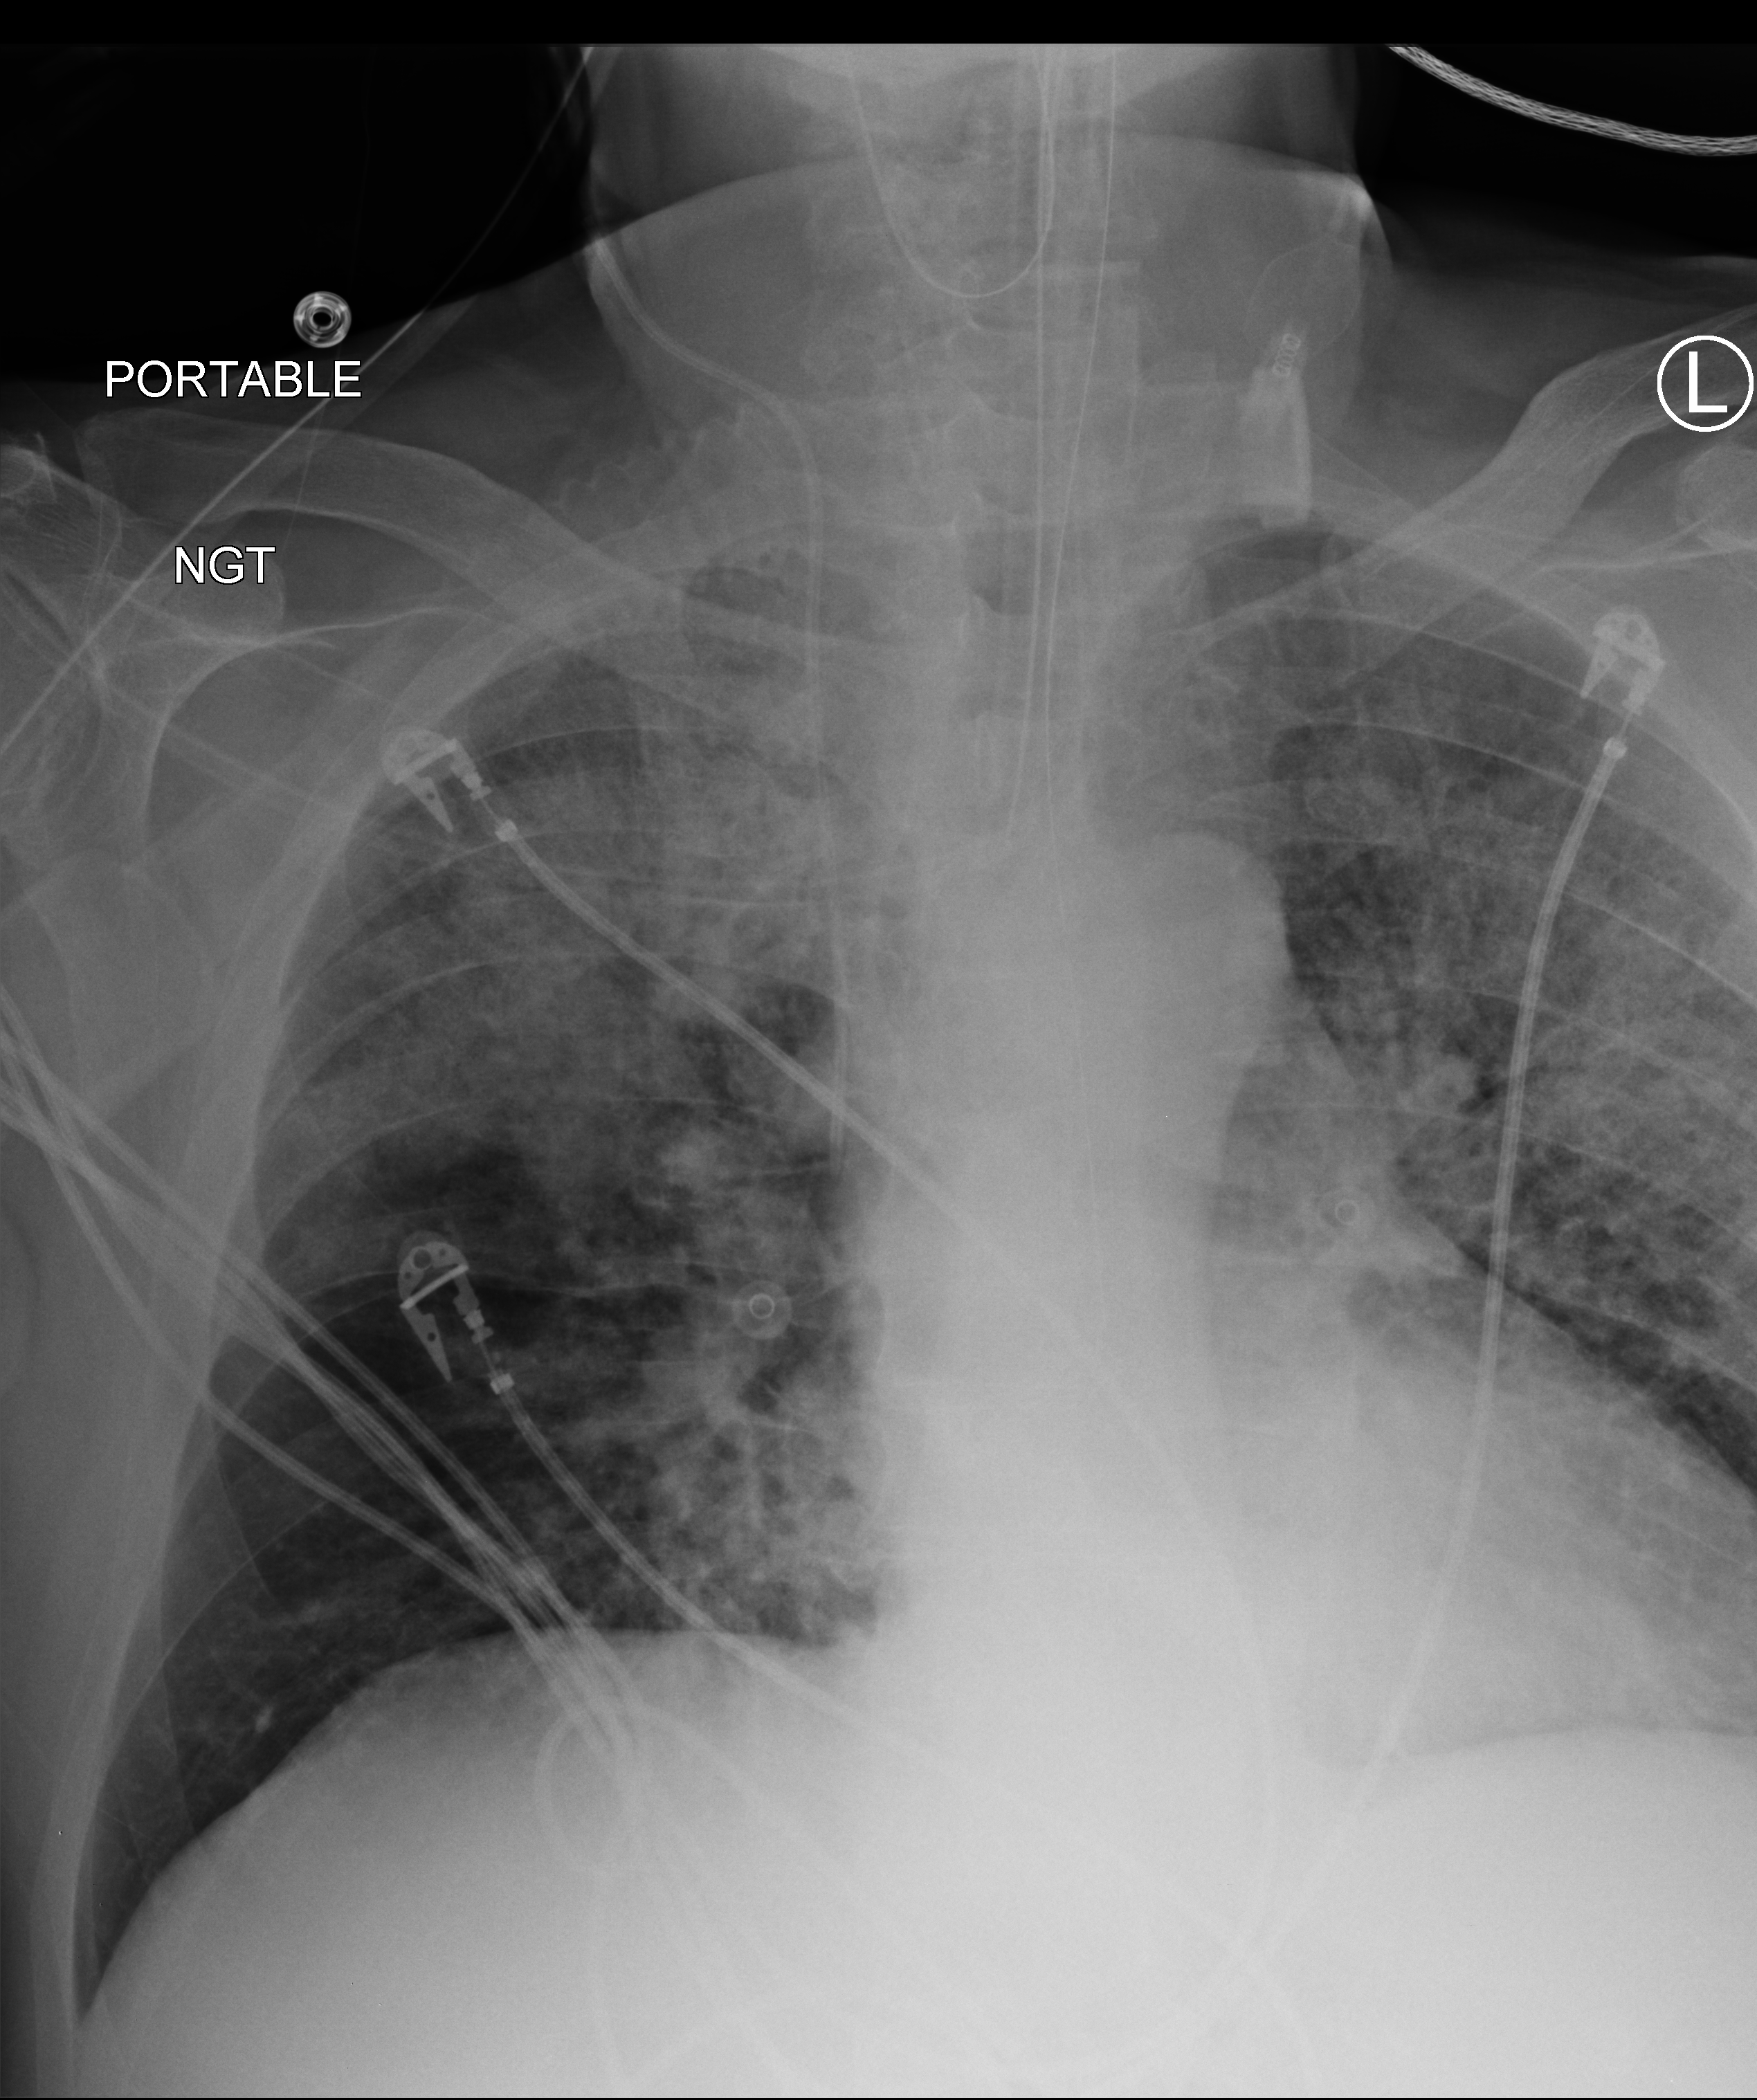
Bedside chest radiograph (computed radiography). Patient hospitalised with COVID-19; male, aged 75–90 years.
From the hospital-stay record, not from the radiograph (when in the stay this image was taken is not recorded): admitted to intensive care during this hospital stay: yes; other chronic lung disease (admission record): yes.